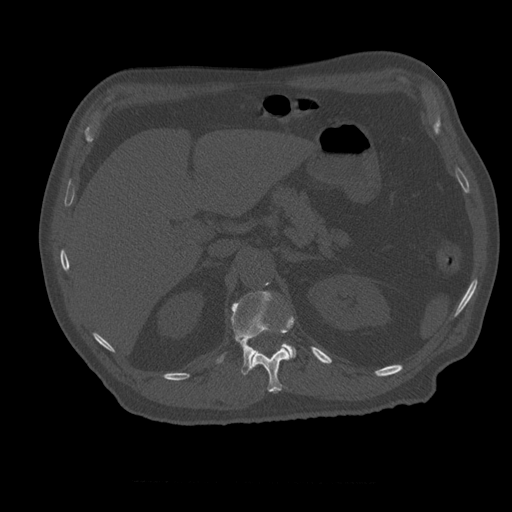
CT including the spine, one axial slice; position 251 of 399 along the scan axis; bone window (W 1800 / L 400 HU); 1.25 mm slice thickness; 512 × 512 image matrix. Patient age 73 years. Case-level facts recorded for this patient, not image findings: primary cancer: prostate; vertebrae with lytic lesions (as recorded): L2.
Annotated regions visible in this slice (semi-automatic segmentation, software-assisted and operator-edited):
- L1 vertebra: box from (x=217, y=291) to (x=297, y=375) px
- T12 vertebra: (x=251, y=317)–(x=294, y=393)